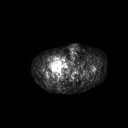
FDG PET of an extremity soft-tissue mass (from a PET/CT study), one axial slice. Slice 288 of 311 in the series (ordered by position). 128 × 128 image matrix, field of view 700 × 700 mm. Male patient, age 50 years. Case-level facts recorded for this patient, not image findings: histological type: undifferentiated - pleiomorphic; grade: high; site of the primary tumour: right thigh.
Annotated regions visible in this slice (expert contour drawn on MRI and transferred to this co-registered scan by the dataset authors):
- gross tumour volume including surrounding oedema: bounding box (x1, y1, x2, y2) in pixels: (54, 55, 65, 66)
- gross tumour volume (mass): (55, 57, 63, 65)